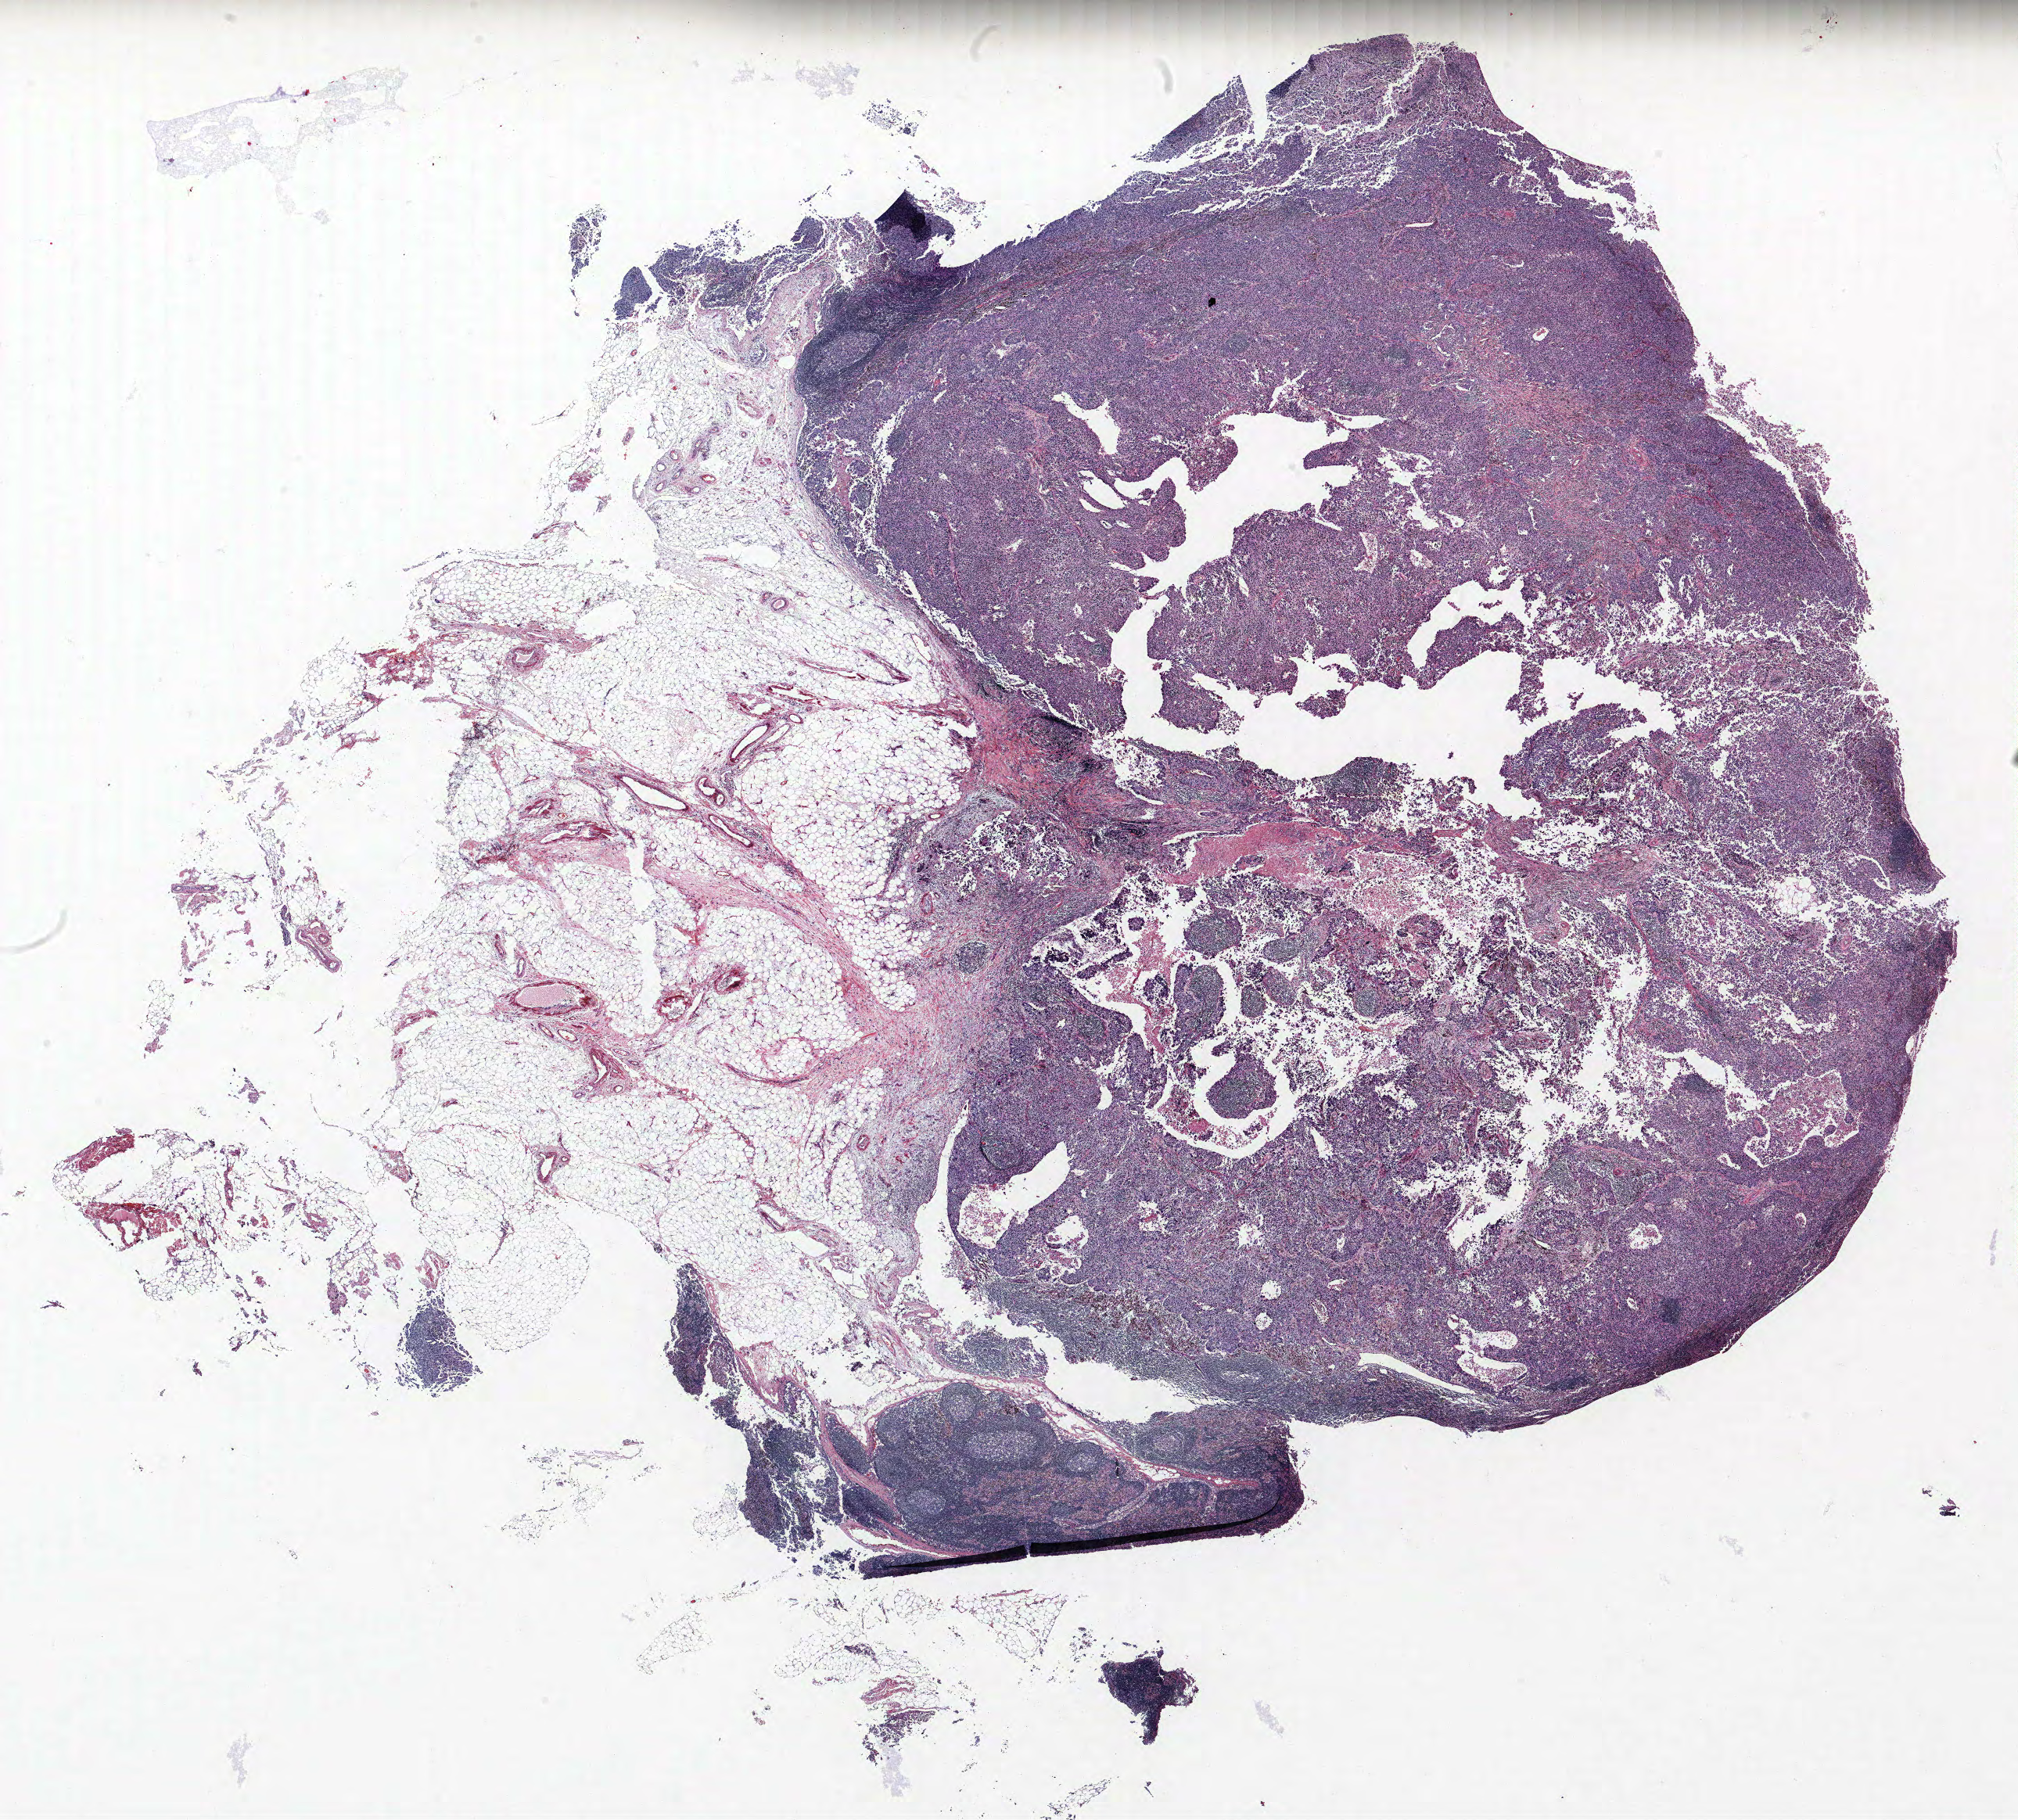
Whole-slide histology image, Hematoxylin and eosin (H&E) stained — a low-resolution overview of the entire scanned area, about 20.6 x 18.6 mm. Formalin-fixed paraffin-embedded (FFPE) section. Lung. Female patient, aged 62 at enrolment. Former smoker at enrolment.
Participant's lung-cancer diagnosis: Squamous cell carcinoma, NOS (ICD-O-3 8070/3).